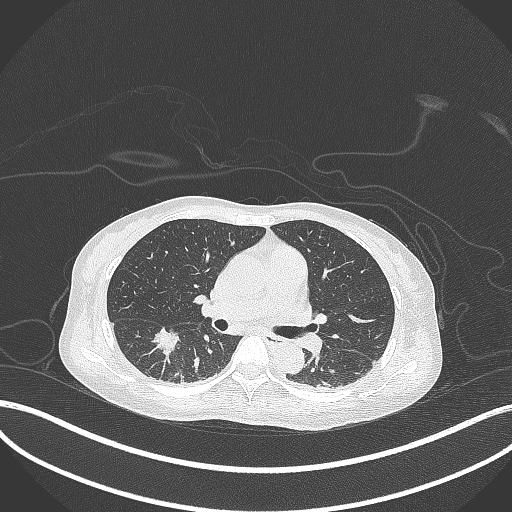
Chest CT, one axial slice. Slice 175 of 261 in the series (ordered by position). Reconstruction kernel B70f. 120 kVp. Lung window (W 1500 / L -600 HU). 1 mm slice thickness. 512 × 512 image matrix. Female patient, age 44 years. Case-level facts recorded for this patient, not image findings: clinical TNM (as recorded): T1c N0 M0.
Outlined on this slice (rectangle marked by the reading radiologist):
- lung tumour (recorded histology: adenocarcinoma): bounding box (x1, y1, x2, y2) in pixels: (151, 325, 179, 357)